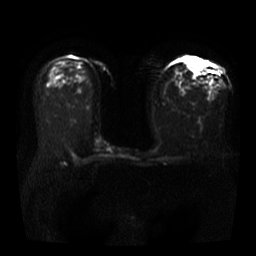
Breast MRI, one axial slice. Position 22 of 40 along the scan axis. Diffusion-weighted series; image 2 of 4 stored at this slice position (different b-values; order by instance number). 3 T. 256 × 256 image matrix, field of view 360 × 360 mm. Female patient.
Annotated regions visible in this slice (expert manual segmentation):
- tumour on diffusion-weighted imaging: bounding box [x1, y1, x2, y2] px = [186, 58, 199, 74]